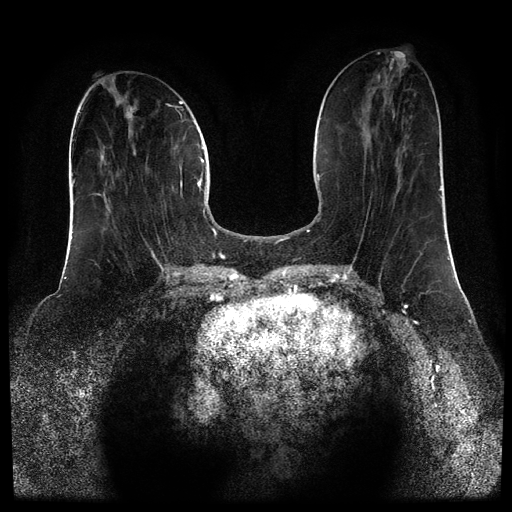
Breast MRI (dynamic contrast-enhanced, multi-phase), one axial slice. Position 34 of 110 along the scan axis. Dynamic contrast-enhanced series, time point 2 of 5 at this slice position (early post-contrast). 1.5 T. TE 2.6 ms, TR 5.4 ms. 512 × 512 image matrix, field of view 340 × 340 mm. Patient: female, 43 years.
Outlined on this slice (semi-automatic segmentation, software-assisted and operator-edited):
- breast lesion (labelled 'tumour' in the annotation; benign lesions carry a separate 'benign' label): box from (x=125, y=106) to (x=137, y=119) px